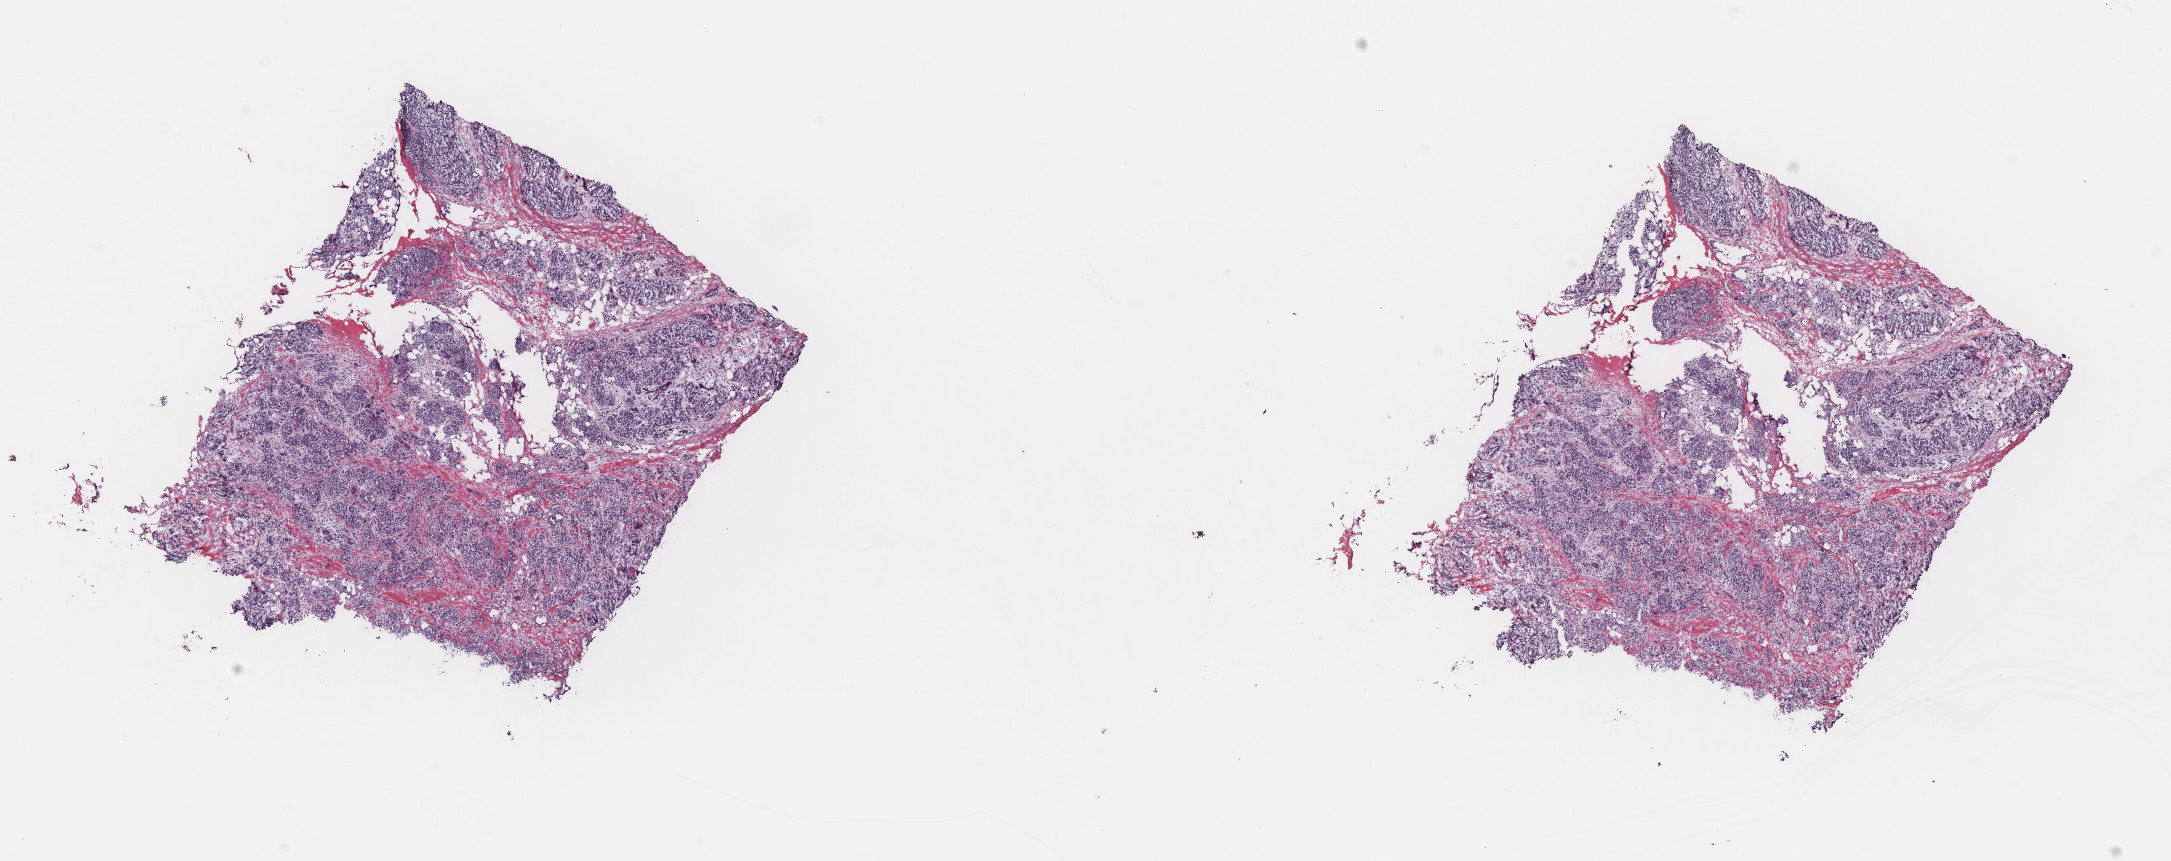
Whole-slide histology image, Hematoxylin and eosin (H&E) stained — low-resolution overview of the scanned area, about 17.2 x 6.8 mm, frozen section from the top of the tissue portion, breast, primary tumour sample. Patient: female, age at initial diagnosis 50 years. Pathologist review of this section (percent, as recorded): tumour cells 75%, tumour nuclei 80%, normal cells 3%, stromal cells 22%, necrosis 0%. Inflammatory infiltration, as recorded: lymphocyte infiltration 3%, monocyte infiltration 0%, neutrophil infiltration 0%.
Lymph nodes positive (case pathology): 0 of 4 examined. AJCC pathologic stage: I (6th edition). Diagnosis: Infiltrating duct carcinoma, NOS.